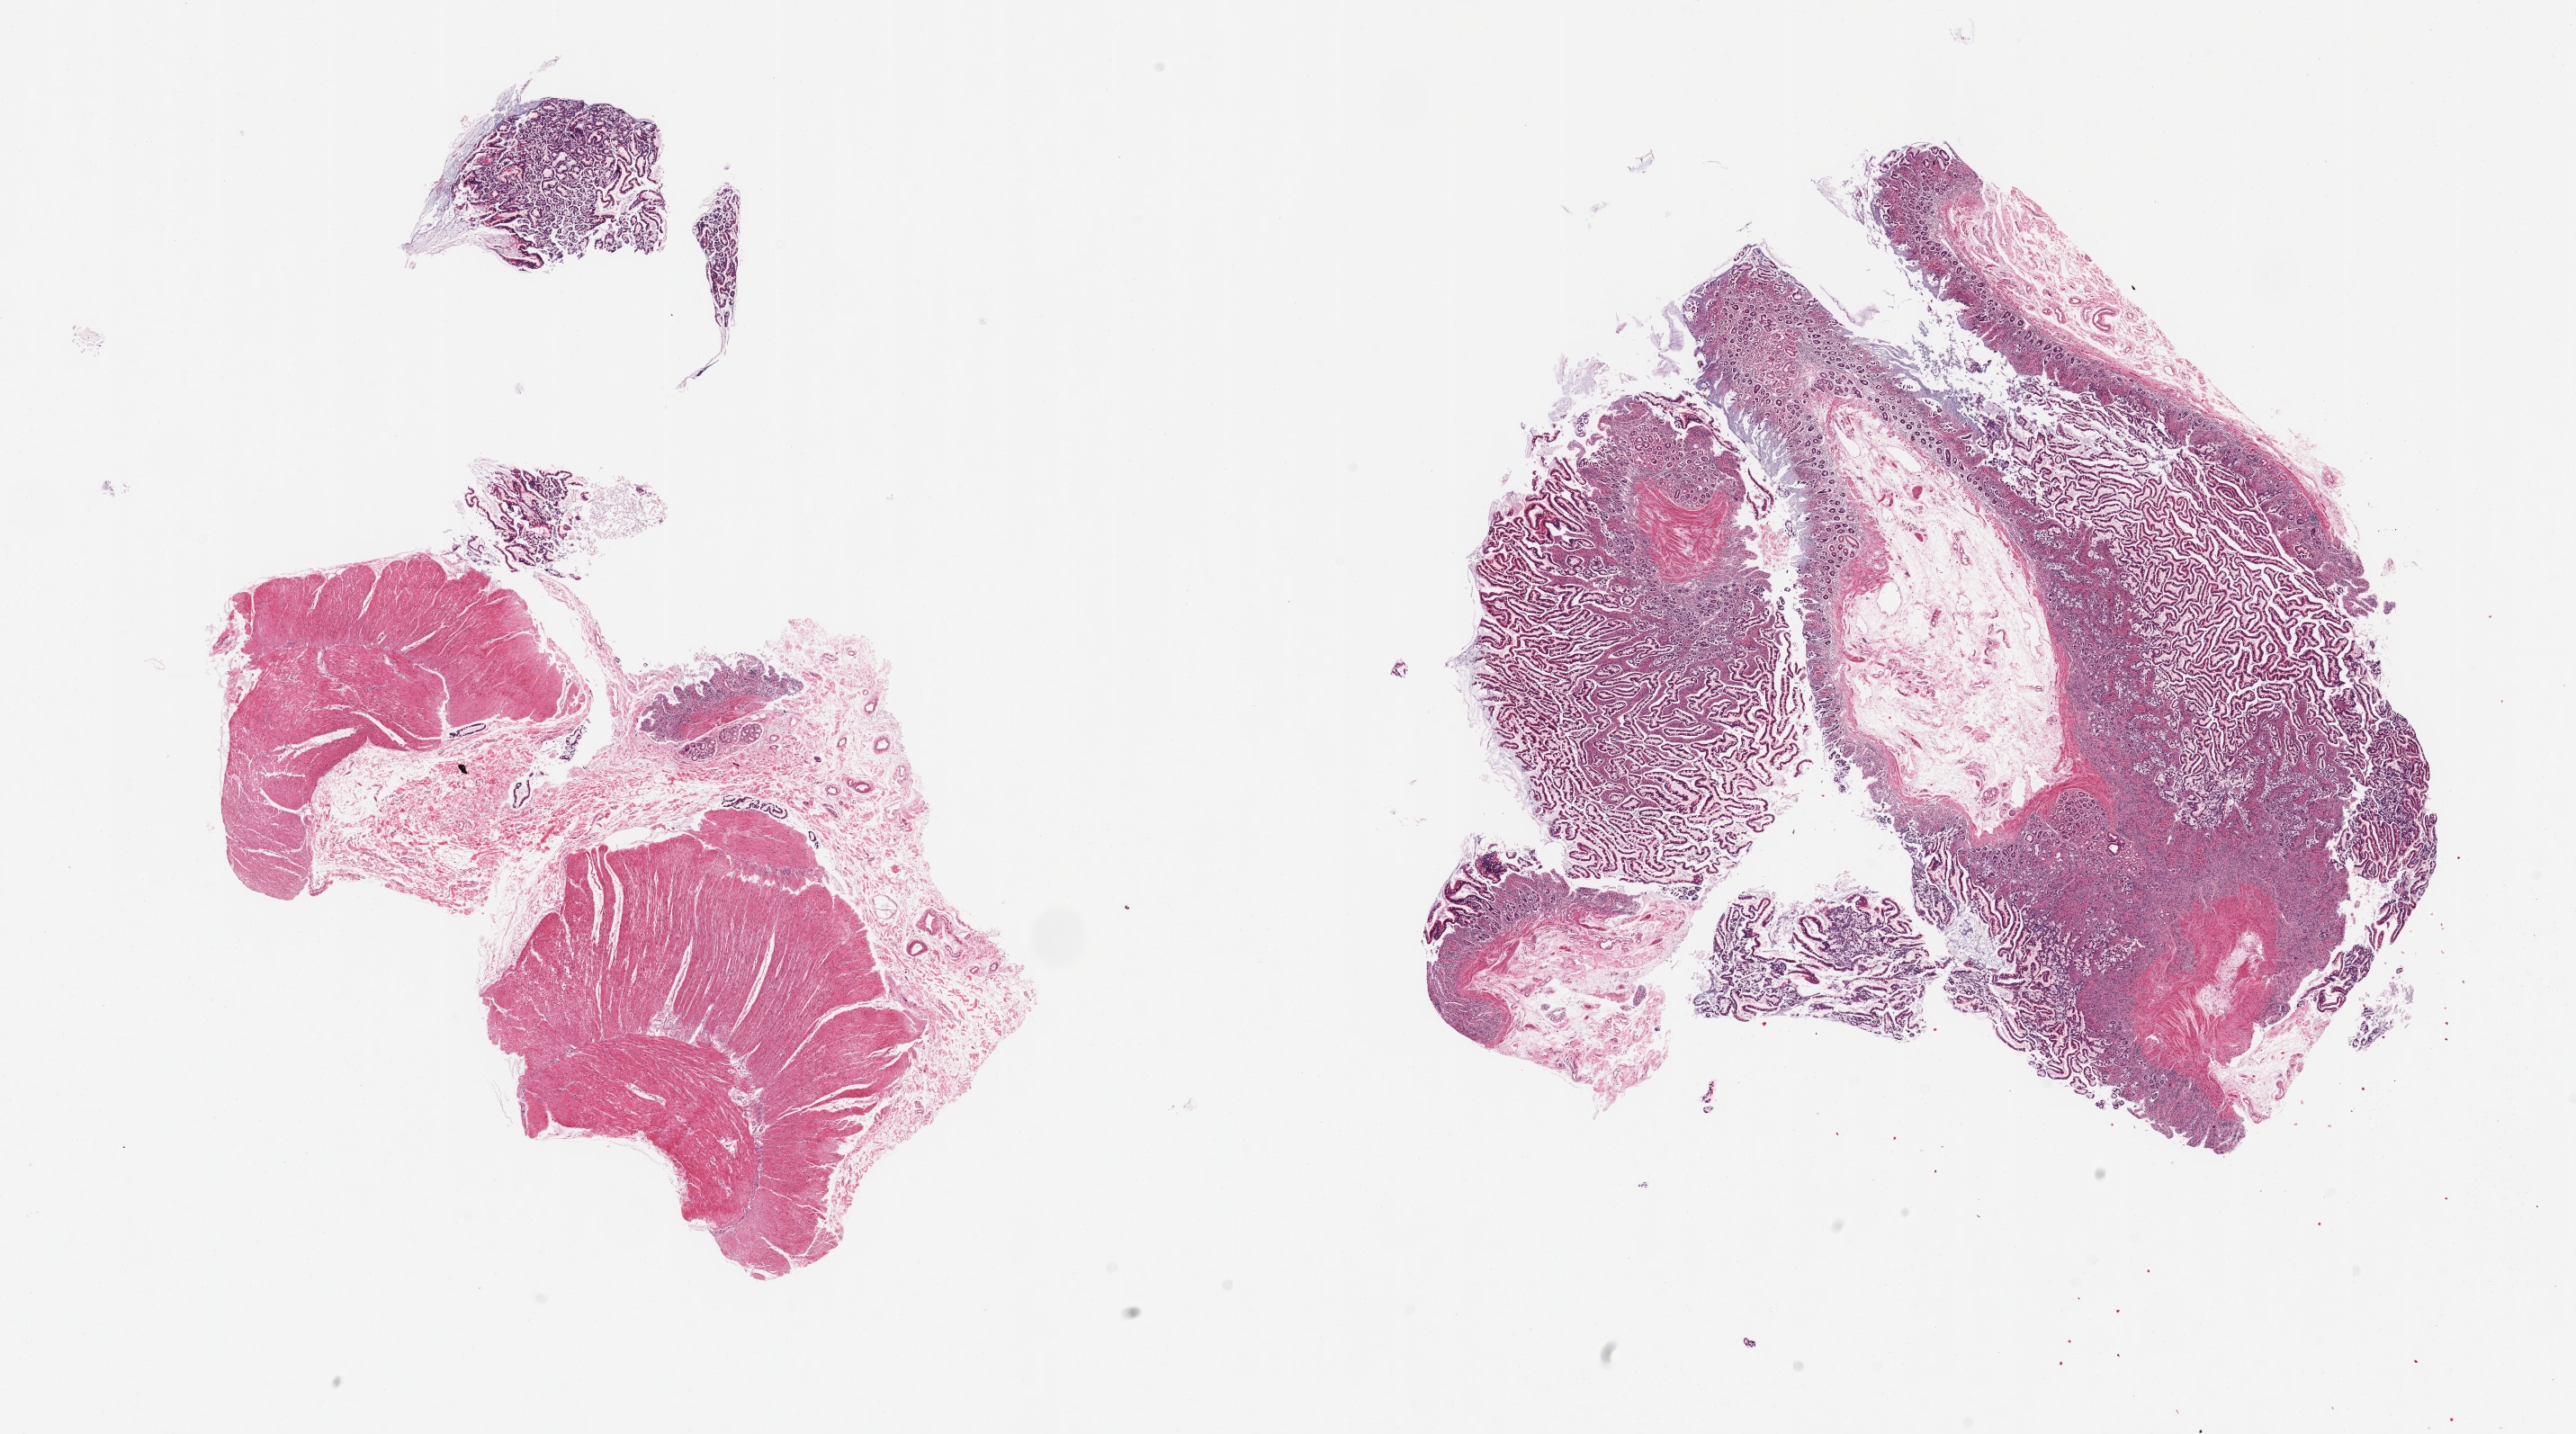
Digitized haematoxylin and eosin-stained section, brightfield — shown as a low-resolution overview of the whole scanned area (about 22.6 x 12.6 mm), PAXgene-fixed paraffin-embedded (PFPE) section, section of pancreas (target tissue), tissue donor sample.
- reviewer comment on this tissue sample: 2 pieces; small intestine sampled no pancreas present